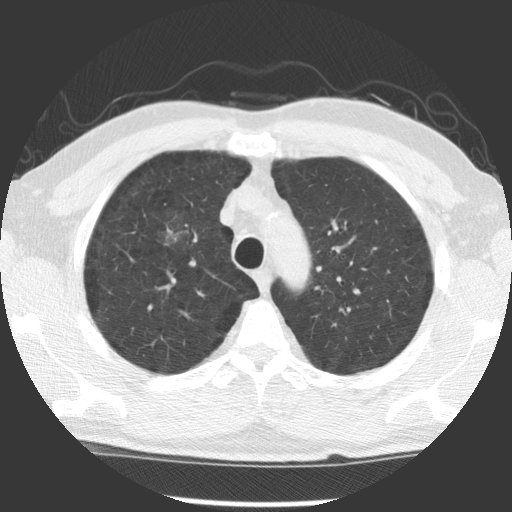
Axial slice from a low-dose chest CT screening exam, first (baseline) screen, lung window (W 1500 / L -600 HU), slice 89 of 122 in the series. Male, age 60 years at enrolment. Former smoker at enrolment.
Lesion marked by an expert reader, box from (x=140, y=208) to (x=207, y=262) px. Reader record for this screening exam (exam-level; its link to the box is not recorded): non-calcified nodule or mass ≥4 mm, right middle lobe, 20 × 20 mm, poorly defined margins, ground glass attenuation. Lung cancer was diagnosed 863 days after this screen: papillary adenocarcinoma, NOS, right upper lobe, moderately differentiated (G2), stage IB (AJCC 6th edition), 32 mm at pathology.